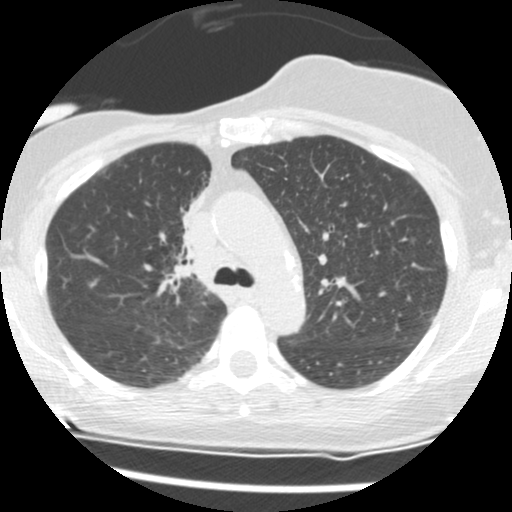
Chest CT (low-dose screening protocol), one axial image. Second annual screen. Lung window (W 1500 / L -600 HU). 2.5 mm slice thickness. Standard (soft-tissue) reconstruction kernel (STANDARD). 120 kVp. Slice 43 of 165 in the series. Female, age 56 years at enrolment. Current smoker at enrolment.
• Lesion marked by an expert reader, bounding box (x1, y1, x2, y2) in pixels: (154, 188, 212, 271).
• The screening reader recorded 2 non-calcified nodules or masses ≥4 mm on this exam (right middle lobe, right lower lobe); which of them this box marks is not recorded.
• Official screen result: positive, change unspecified: nodule(s) >= 4 mm or enlarging nodule(s), mass(es), or other non-specific abnormalities suspicious for lung cancer.